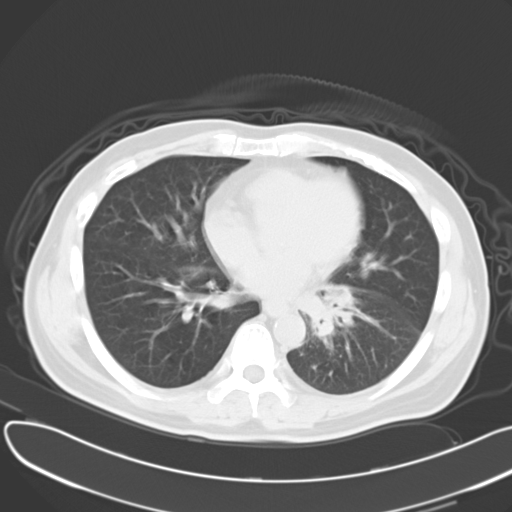
Chest CT, one axial slice; position 14 of 30 along the scan axis; reconstruction kernel B40f; 120 kVp; lung window (W 1500 / L -600 HU); 10 mm slice thickness; 512 × 512 image matrix. Patient: male, 55 years. From the clinical record (not read from this slice): clinical TNM (as recorded): T2 N3 M0; histopathological grade: G3.
Outlined on this slice (rectangle marked by the reading radiologist):
- lung tumour (recorded histology: small cell carcinoma): bounding box [x1, y1, x2, y2] px = [289, 271, 360, 348]